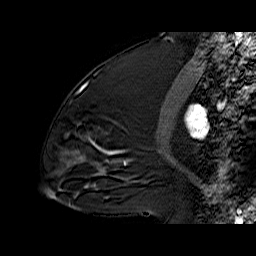
Breast MRI (dynamic contrast-enhanced), one sagittal slice; slice 30 of 60 in the series (ordered by position); dynamic contrast-enhanced series, time point 2 of 6 at this slice position (early post-contrast); 1.5 T; TE 6.3 ms, TR 32.9 ms; 4 mm slice thickness; 256 × 256 image matrix, field of view 200 × 200 mm. Female patient. From the clinical record (not read from this slice): setting: breast cancer imaged before/during neoadjuvant chemotherapy; receptor status: triple-negative.
Annotated regions visible in this slice (semi-automatically segmented with operator editing):
- analysis volume of interest (the breast-tissue region the enhancement analysis was run in; not a lesion): box from (x=68, y=76) to (x=117, y=170) px
- tumour enhancement mask (voxels above the 100 % enhancement threshold inside the analysis volume of interest): (x=98, y=147)–(x=115, y=155)